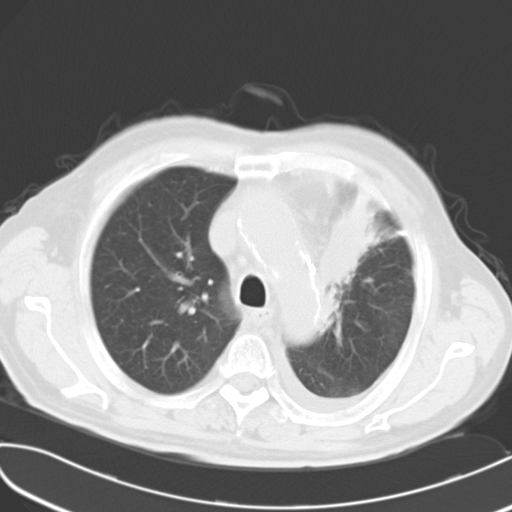
Chest CT, one axial slice; slice 20 of 27 in the series (ordered by position); lung window (W 1500 / L -600 HU); 10 mm slice thickness; 512 × 512 image matrix. Male patient, age 70 years. From the clinical record (not read from this slice): clinical TNM (as recorded): T2 N1 M3; histopathological grade: G3.
Structures marked on this image (rectangle marked by the reading radiologist):
- lung tumour (recorded histology: small cell carcinoma): bounding box <329,175,395,339> (left, top, right, bottom; pixels)